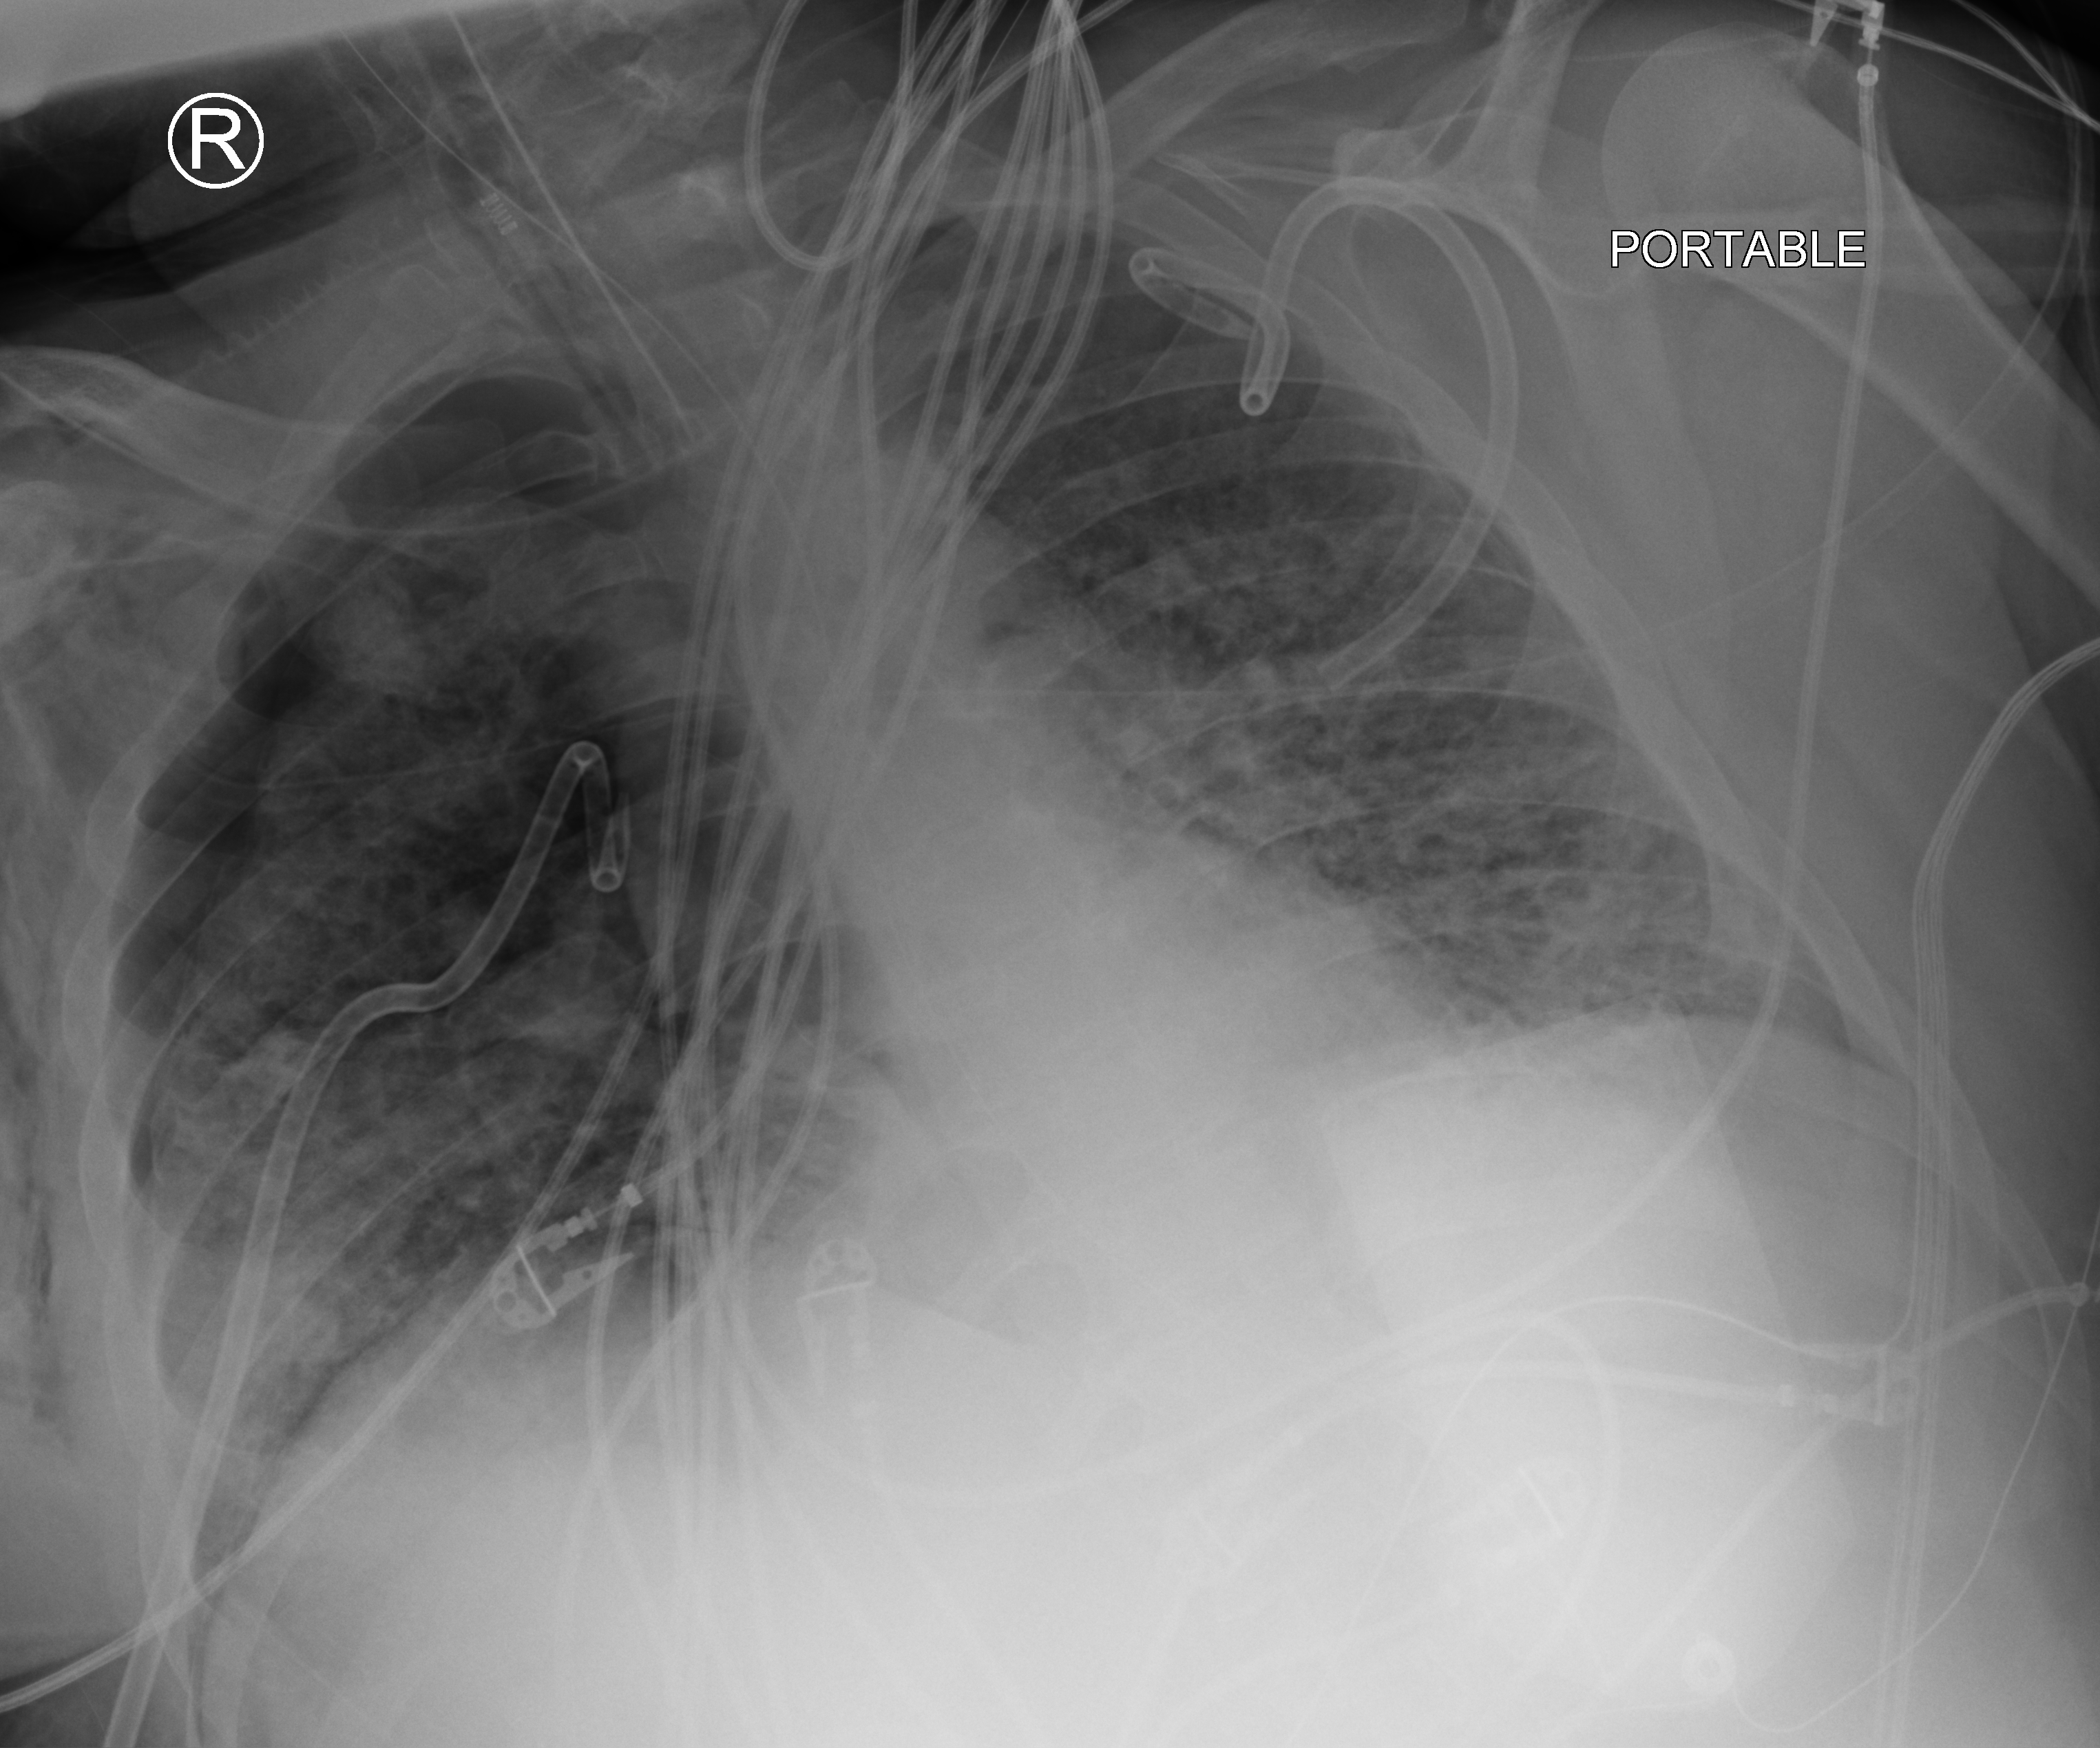
Bedside chest radiograph (computed radiography). Patient hospitalised with COVID-19, aged 18–59 years.
Hospital-stay facts (about this admission, not read from this image; timing relative to this image not recorded):
- mechanically ventilated during this hospital stay: yes
- admitted to intensive care during this hospital stay: yes
- length of hospital stay: 31 days